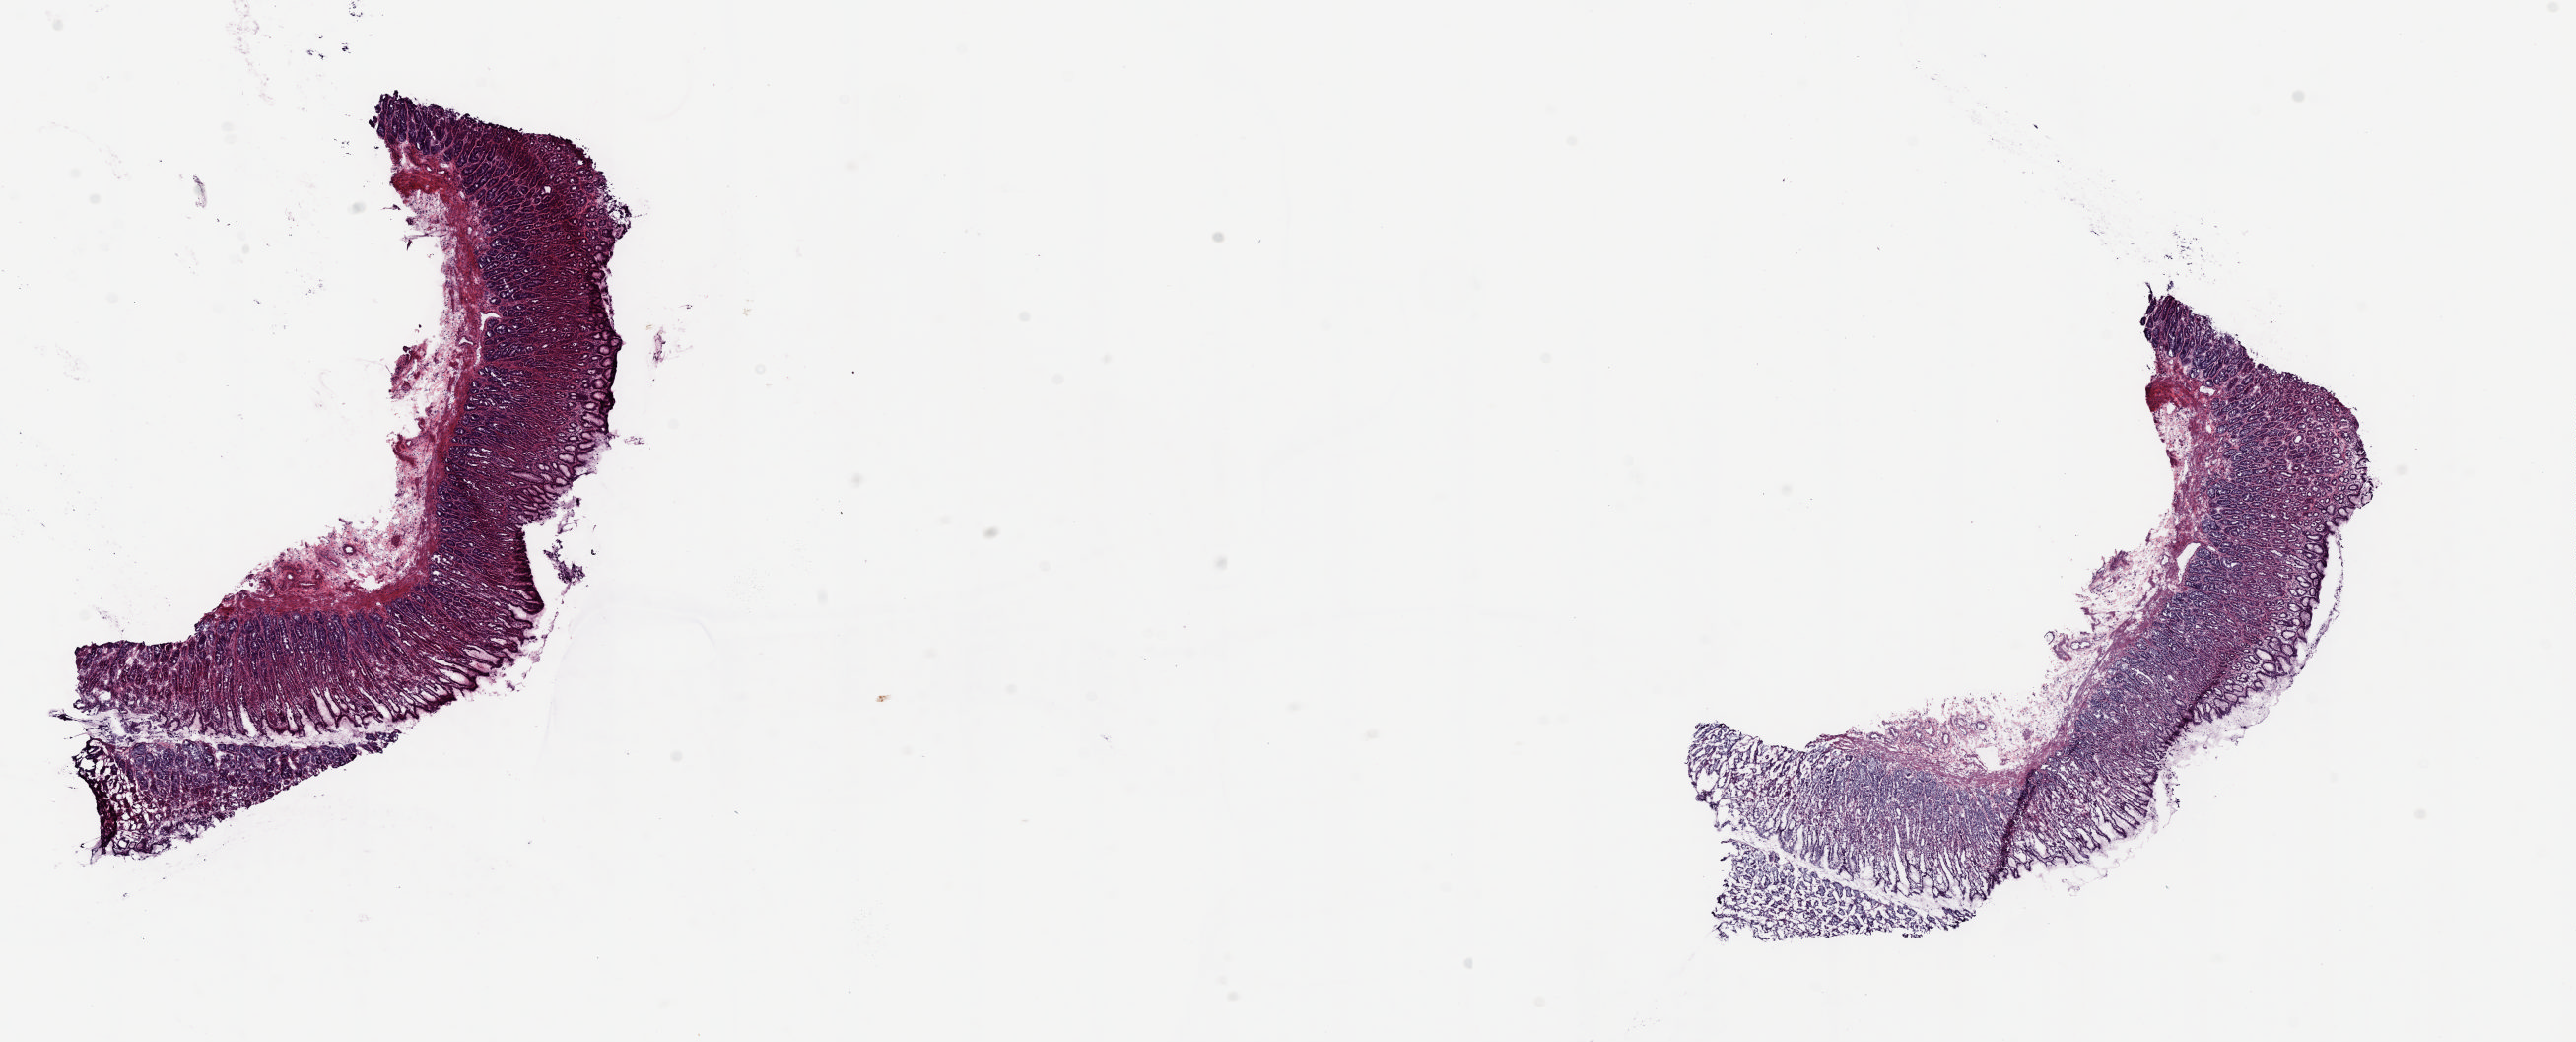
Whole-slide histology image, H&E, a low-resolution overview of the entire scanned area, about 20.7 x 8.4 mm (slide scanned at 20x), frozen section from the top of the tissue portion, solid tissue normal (non-tumour tissue) sample from the esophagus. Male patient; age at initial diagnosis 75 years. Pathologist review of this section (percent, as recorded): tumour cells 0%, tumour nuclei 0%, normal cells 100%, stromal cells 0%, necrosis 0%. Infiltration values recorded for this section: lymphocyte infiltration 1%, monocyte infiltration 0%, neutrophil infiltration 0%.
* this section: solid tissue normal sample (biorepository sample class)
* patient diagnosis: Squamous cell carcinoma, NOS (middle third of esophagus)